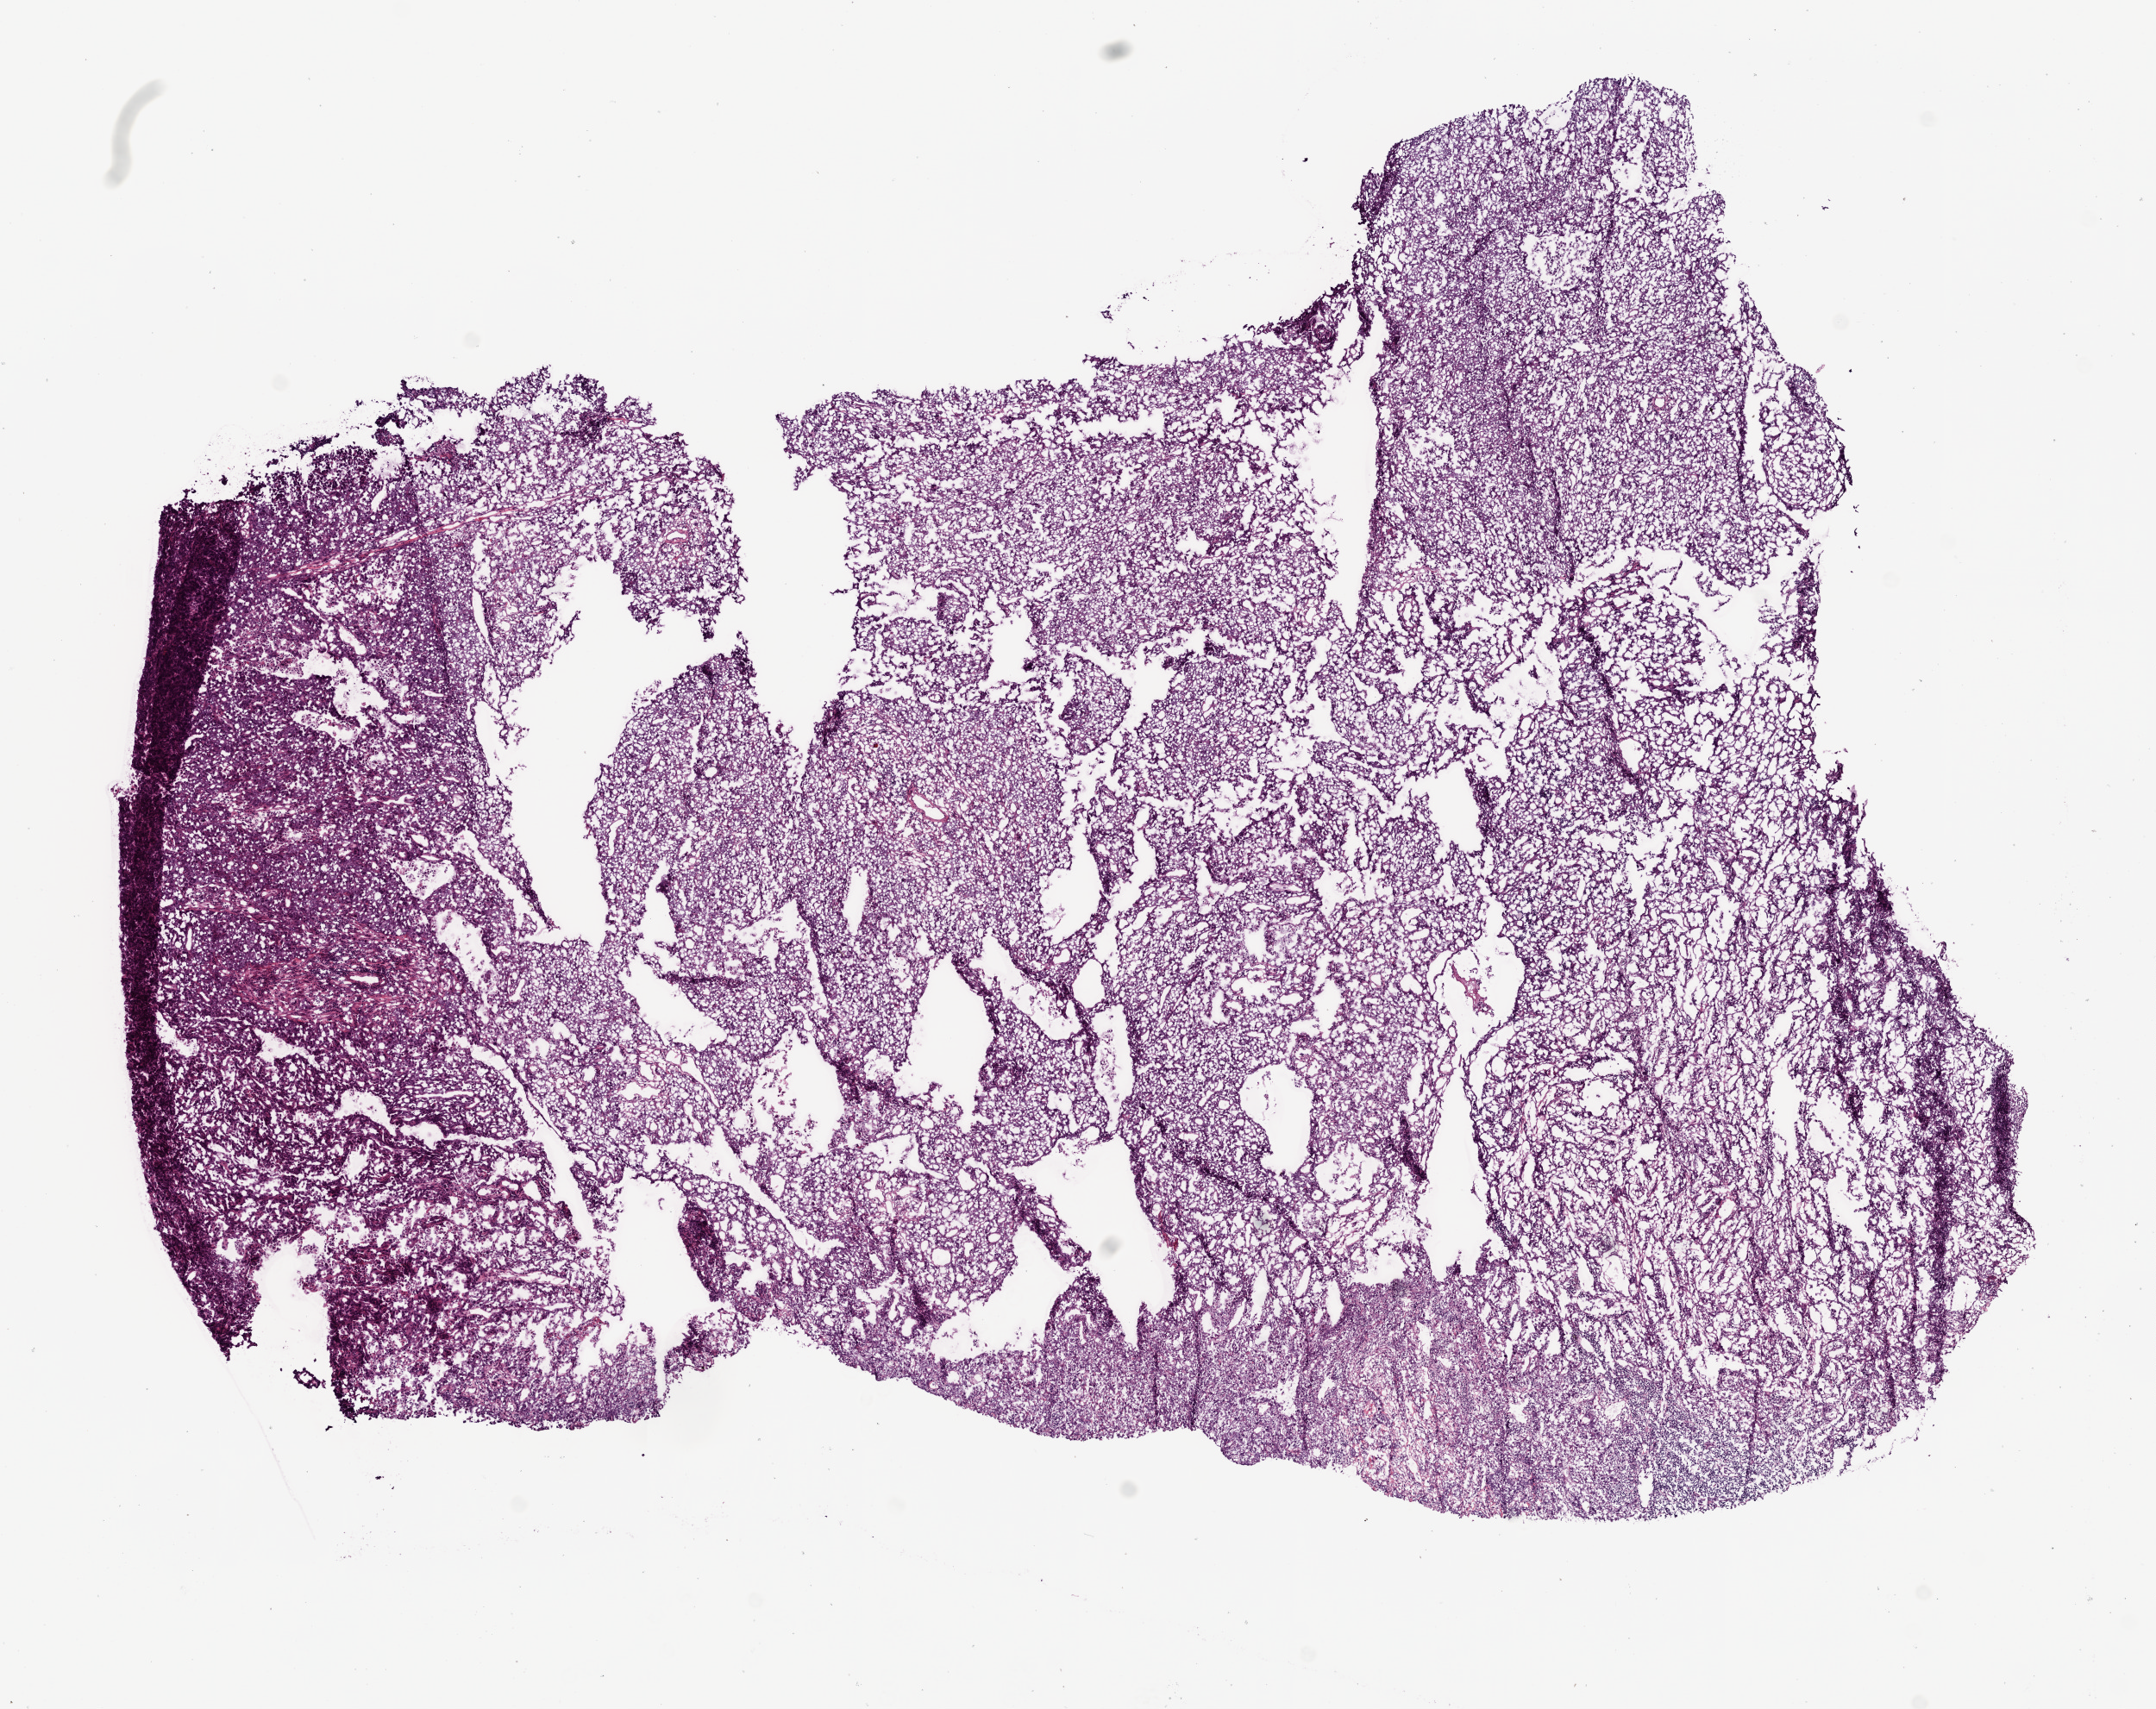
Digitized H&E tissue section (whole slide) — low-resolution overview of the scanned area, about 10.0 x 8.0 mm (from a 20x scan); frozen section from the bottom of the tissue portion; sample: primary tumour, lung. Male, age 40 years at initial diagnosis. Slide review estimates, as recorded: tumour cells 95%, tumour nuclei 80%, normal cells 0%, stromal cells 5%, necrosis 0%.
AJCC pathologic stage: IB. Laterality: right. Histologic diagnosis: Squamous cell carcinoma, NOS (upper lobe, lung).